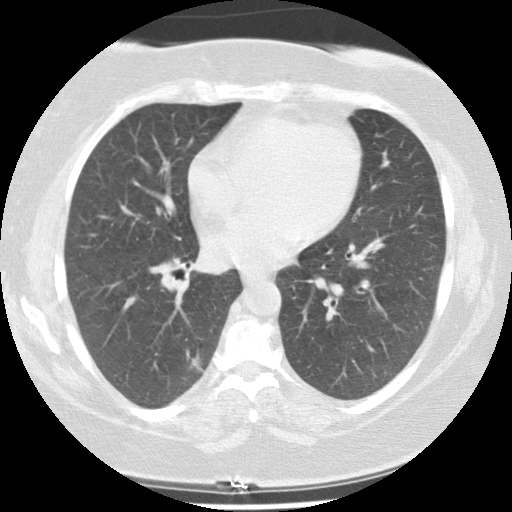
Low-dose screening chest CT, one axial slice; slice 72 of 131 in the series (ordered by position); reconstruction kernel STANDARD; 140 kVp; lung window (W 1500 / L -600 HU); 2.5 mm slice thickness; 512 × 512 image matrix, field of view 320 × 320 mm.
Annotated regions visible in this slice (outlined manually by an expert reader):
- lesion 1 (tumor, lower lobe of right lung): bounding box (x1, y1, x2, y2) in pixels: (192, 357, 202, 370)